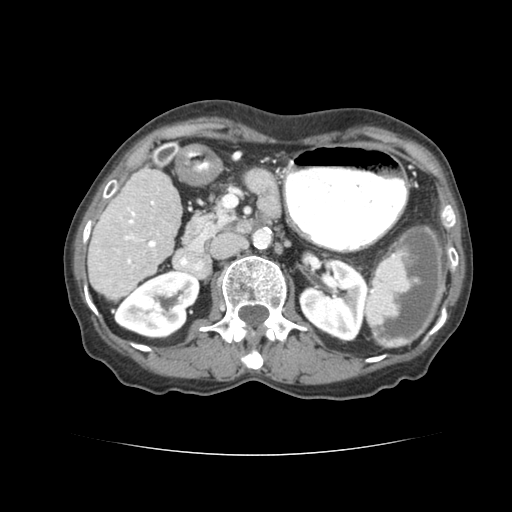
Contrast-enhanced abdominal CT (liver protocol), one axial slice. Position 27 of 77 along the scan axis. Reconstruction kernel STANDARD. 120 kVp. Soft-tissue window (W 400 / L 40 HU). 2.5 mm slice thickness. 512 × 512 image matrix, field of view 340 × 340 mm. Case-level facts recorded for this patient, not image findings: diagnosis: hepatocellular carcinoma (patient treated with transarterial chemoembolisation; whether this scan precedes or follows treatment is not stated here); TNM stage (as recorded): Stage-I.
Annotated regions visible in this slice (semi-automatically segmented with operator editing):
- liver parenchyma outside the tumour (the mass and vessels are separate outlines, so this box may not span the whole liver): bounding box [x1, y1, x2, y2] px = [86, 166, 181, 298]
- liver vessels: [123, 198, 154, 244]